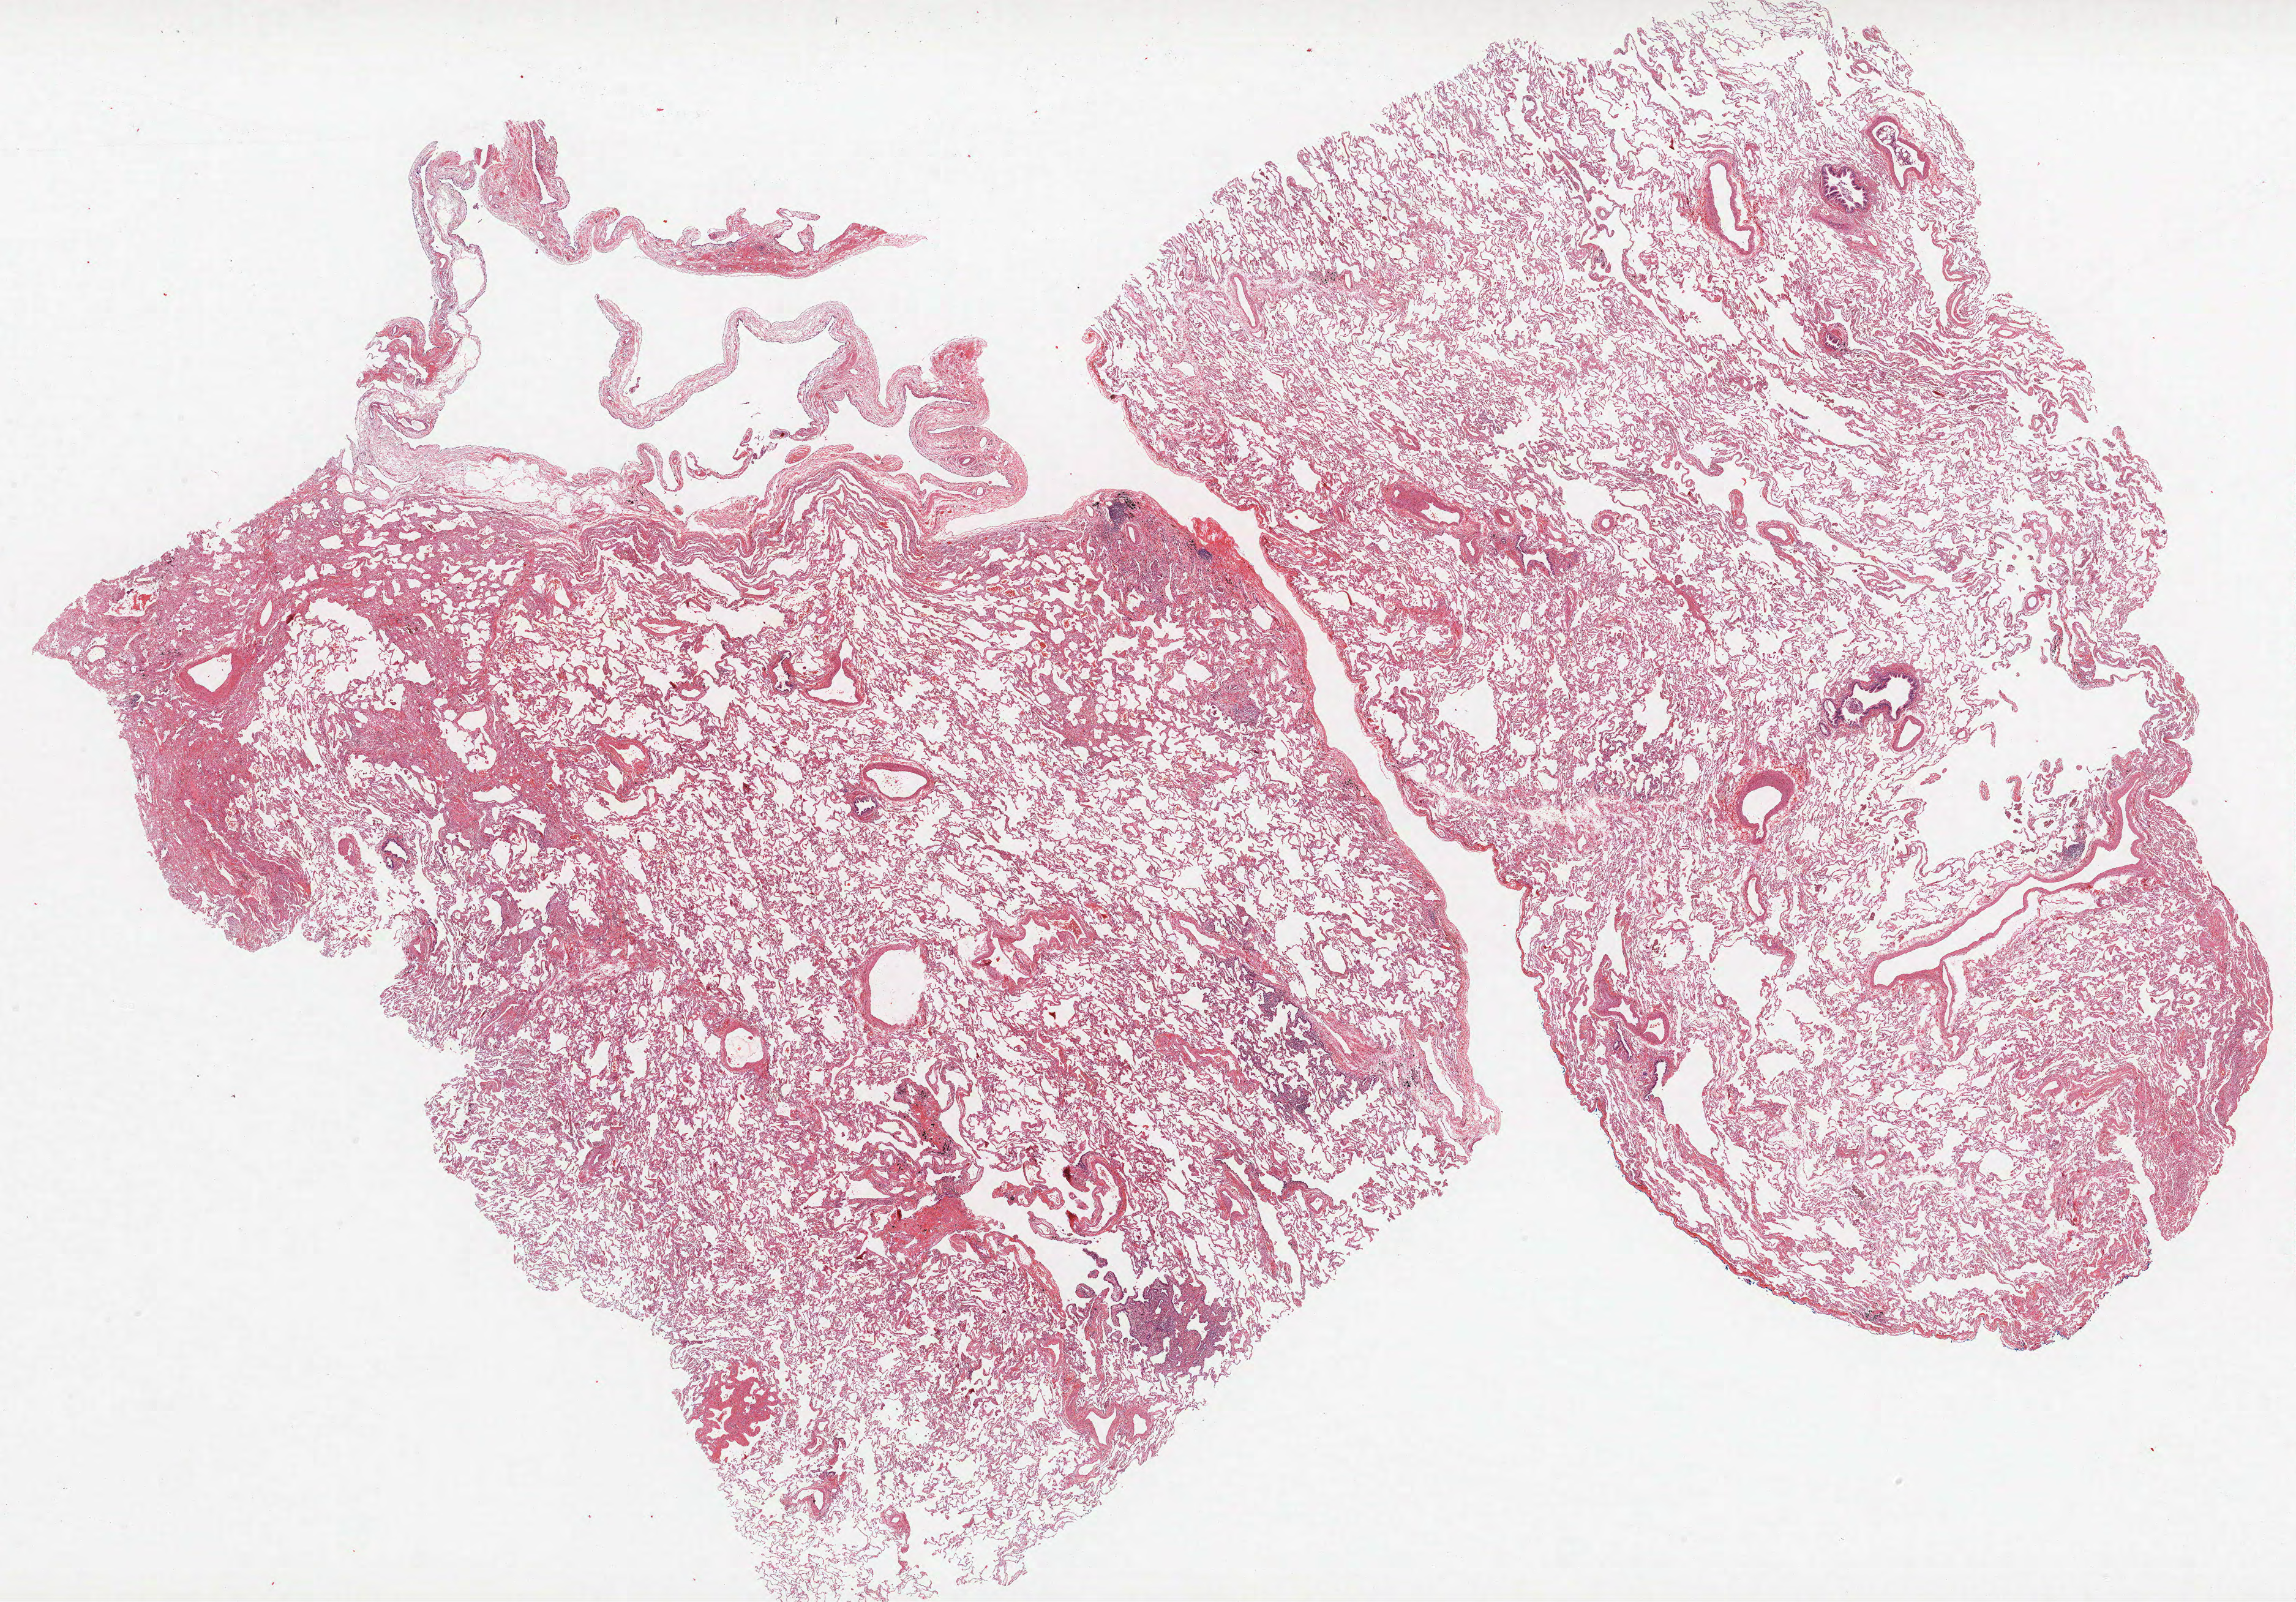
Hematoxylin and eosin (H&E) stained whole-slide image, whole scanned area (about 30.0 x 20.9 mm, from a 40x scan) shown as a low-resolution overview. FFPE section. Lung tissue. Female, age 64 at enrolment. Current smoker at enrolment. Grade: poorly differentiated (G3).
Participant's lung-cancer diagnosis: Adenocarcinoma, NOS. Tumour size (pathology): 15 mm. Stage (AJCC 6th edition): IB. Primary tumour location (clinical record): right upper lobe.